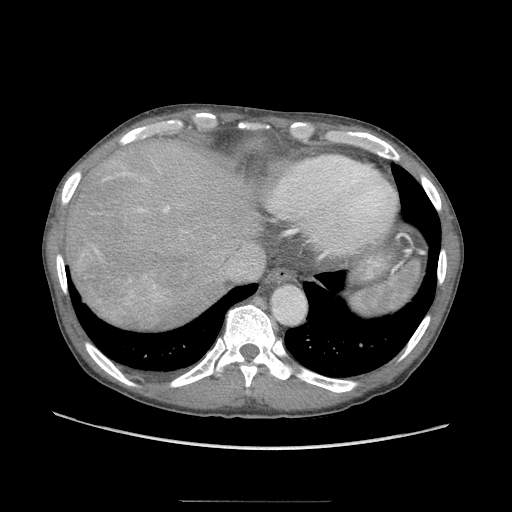
Contrast-enhanced abdominal CT (liver protocol), one axial slice; position 83 of 103 along the scan axis; soft-tissue window (W 400 / L 40 HU); 512 × 512 image matrix, field of view 380 × 380 mm. Case-level facts recorded for this patient, not image findings: diagnosis: hepatocellular carcinoma (patient treated with transarterial chemoembolisation; whether this scan precedes or follows treatment is not stated here); TNM stage (as recorded): Stage-IIIA; Child-Pugh class: A.
Annotated regions visible in this slice (semi-automatic segmentation, software-assisted and operator-edited):
- abdominal aorta: bounding box <273,287,305,323> (left, top, right, bottom; pixels)
- liver parenchyma outside the tumour (the mass and vessels are separate outlines, so this box may not span the whole liver): <66,136,260,328>
- liver vessels: <152,273,228,287>